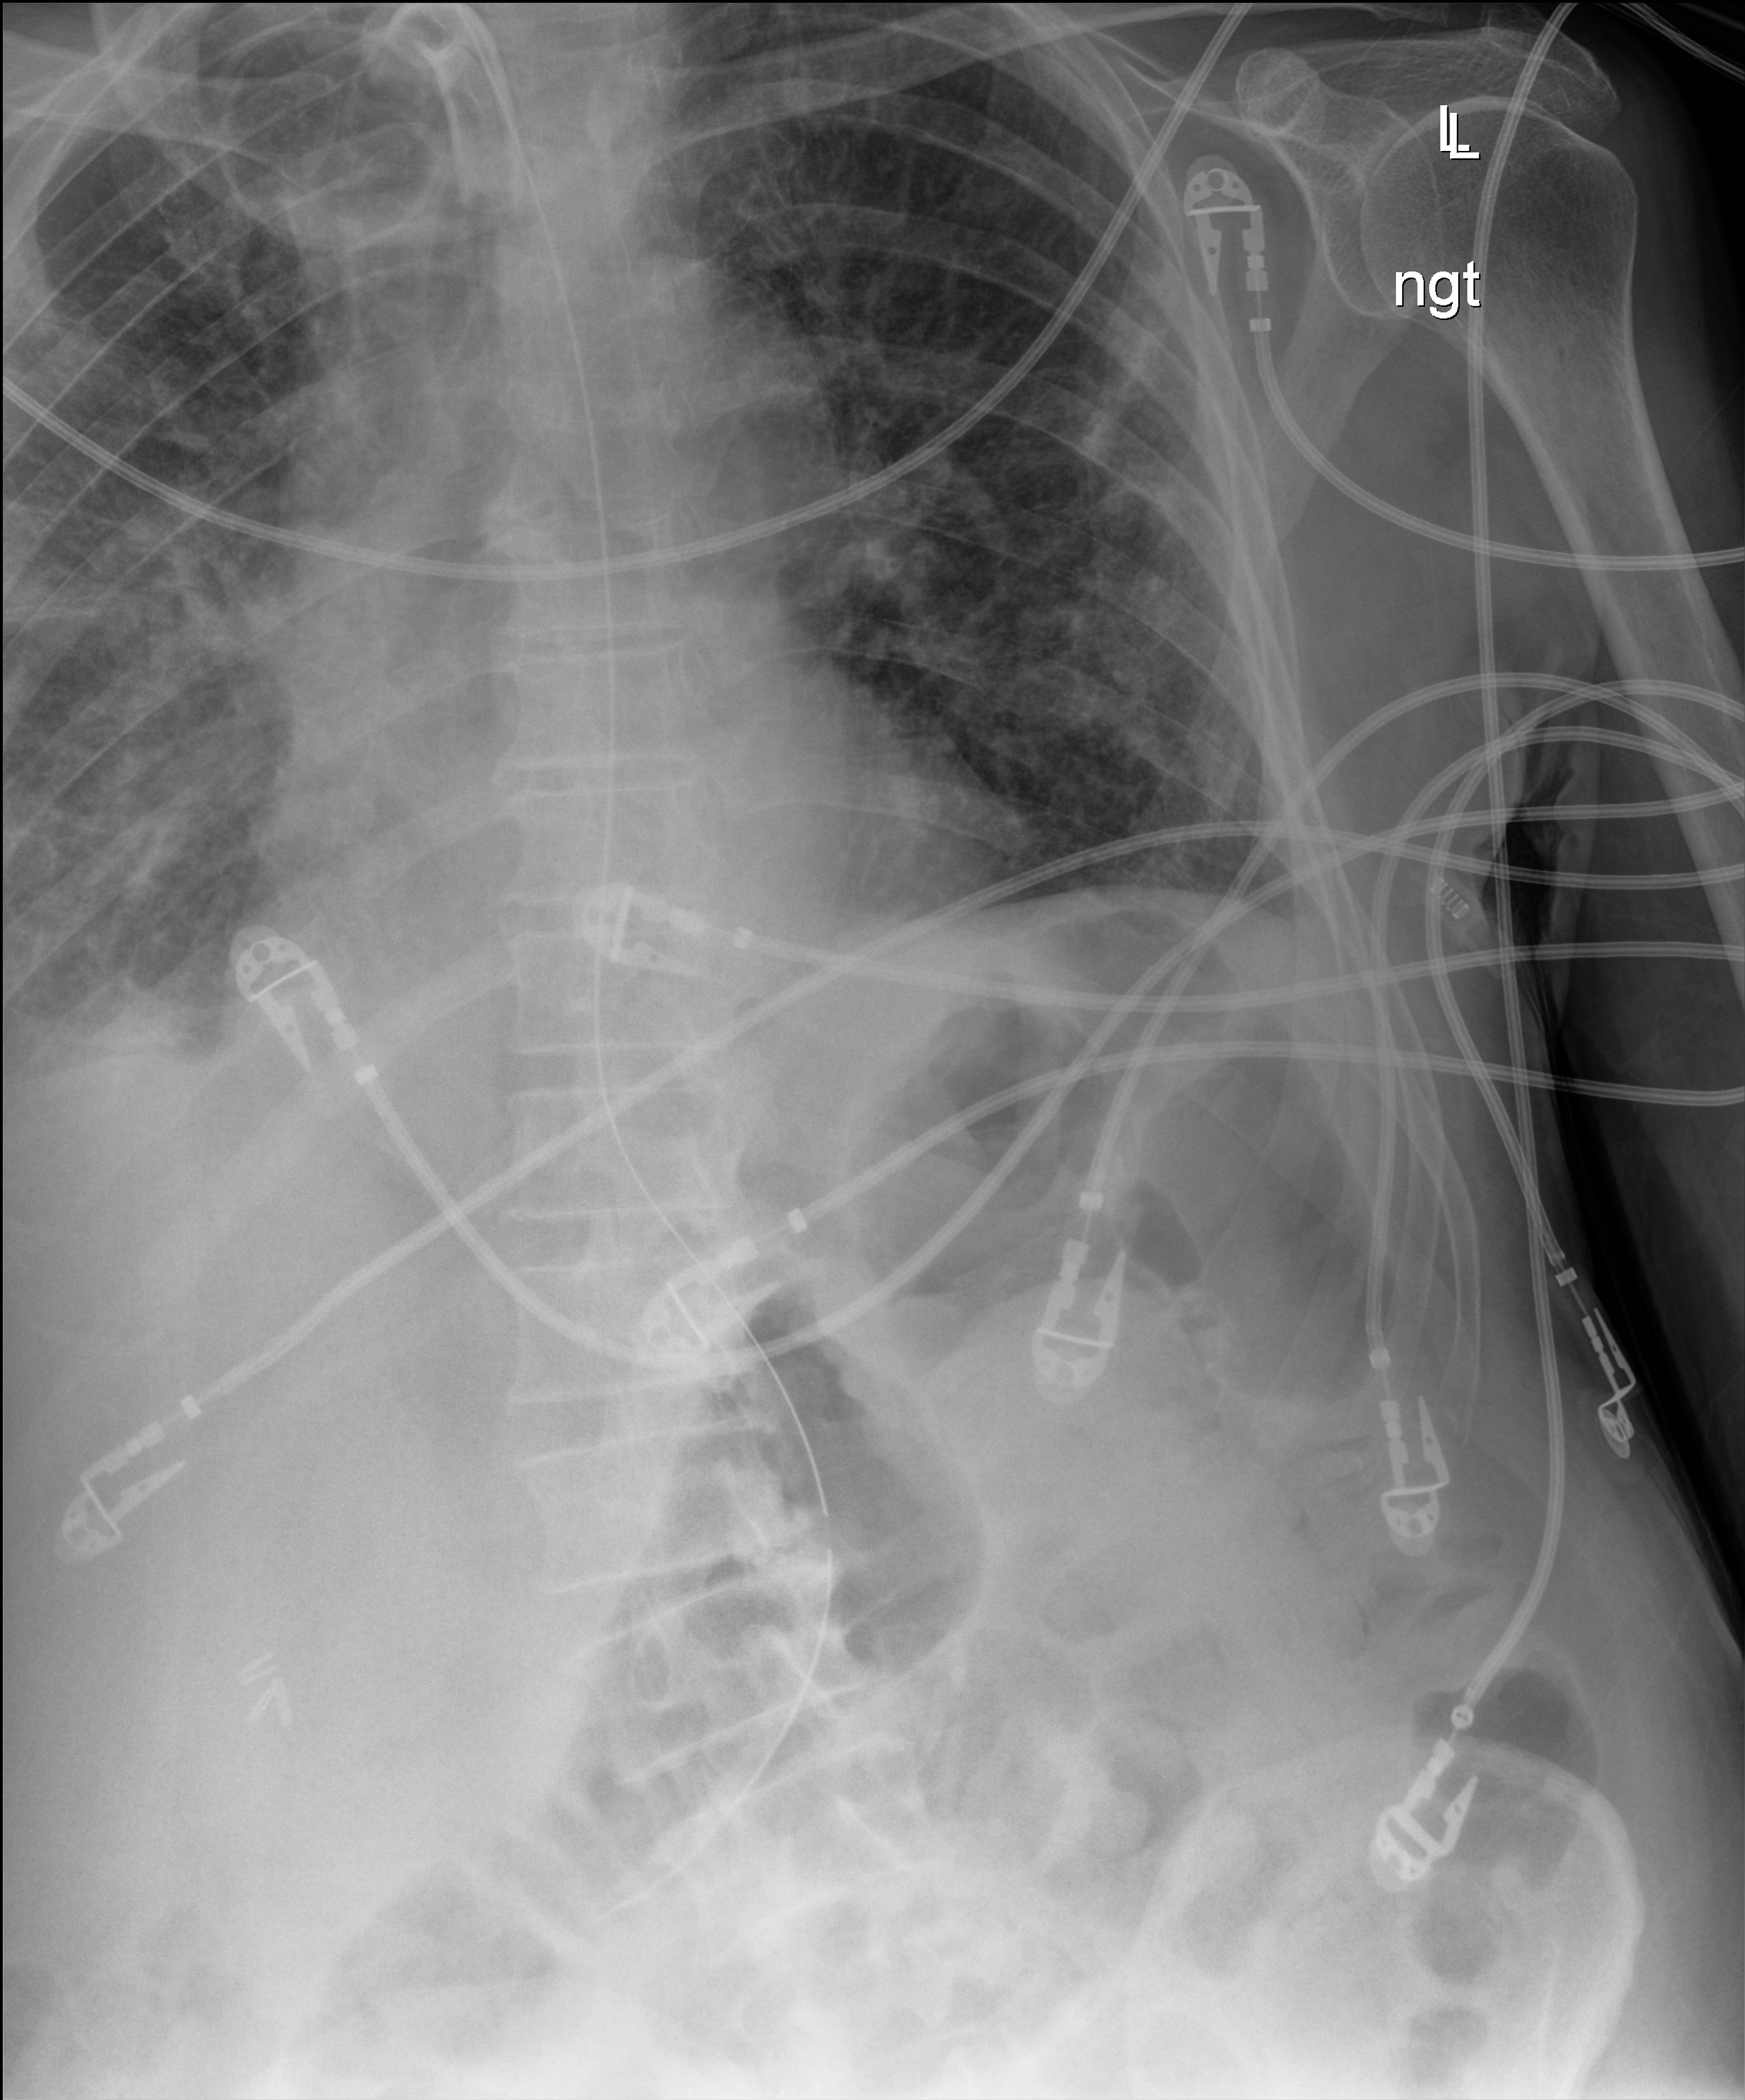
Bedside chest radiograph (digital radiography). Male patient hospitalised with COVID-19, age 75–90 years.
From the hospital-stay record, not from the radiograph (when in the stay this image was taken is not recorded): smoking status (admission record): never; chronic kidney disease (admission record): no; admitted to intensive care during this hospital stay: yes.